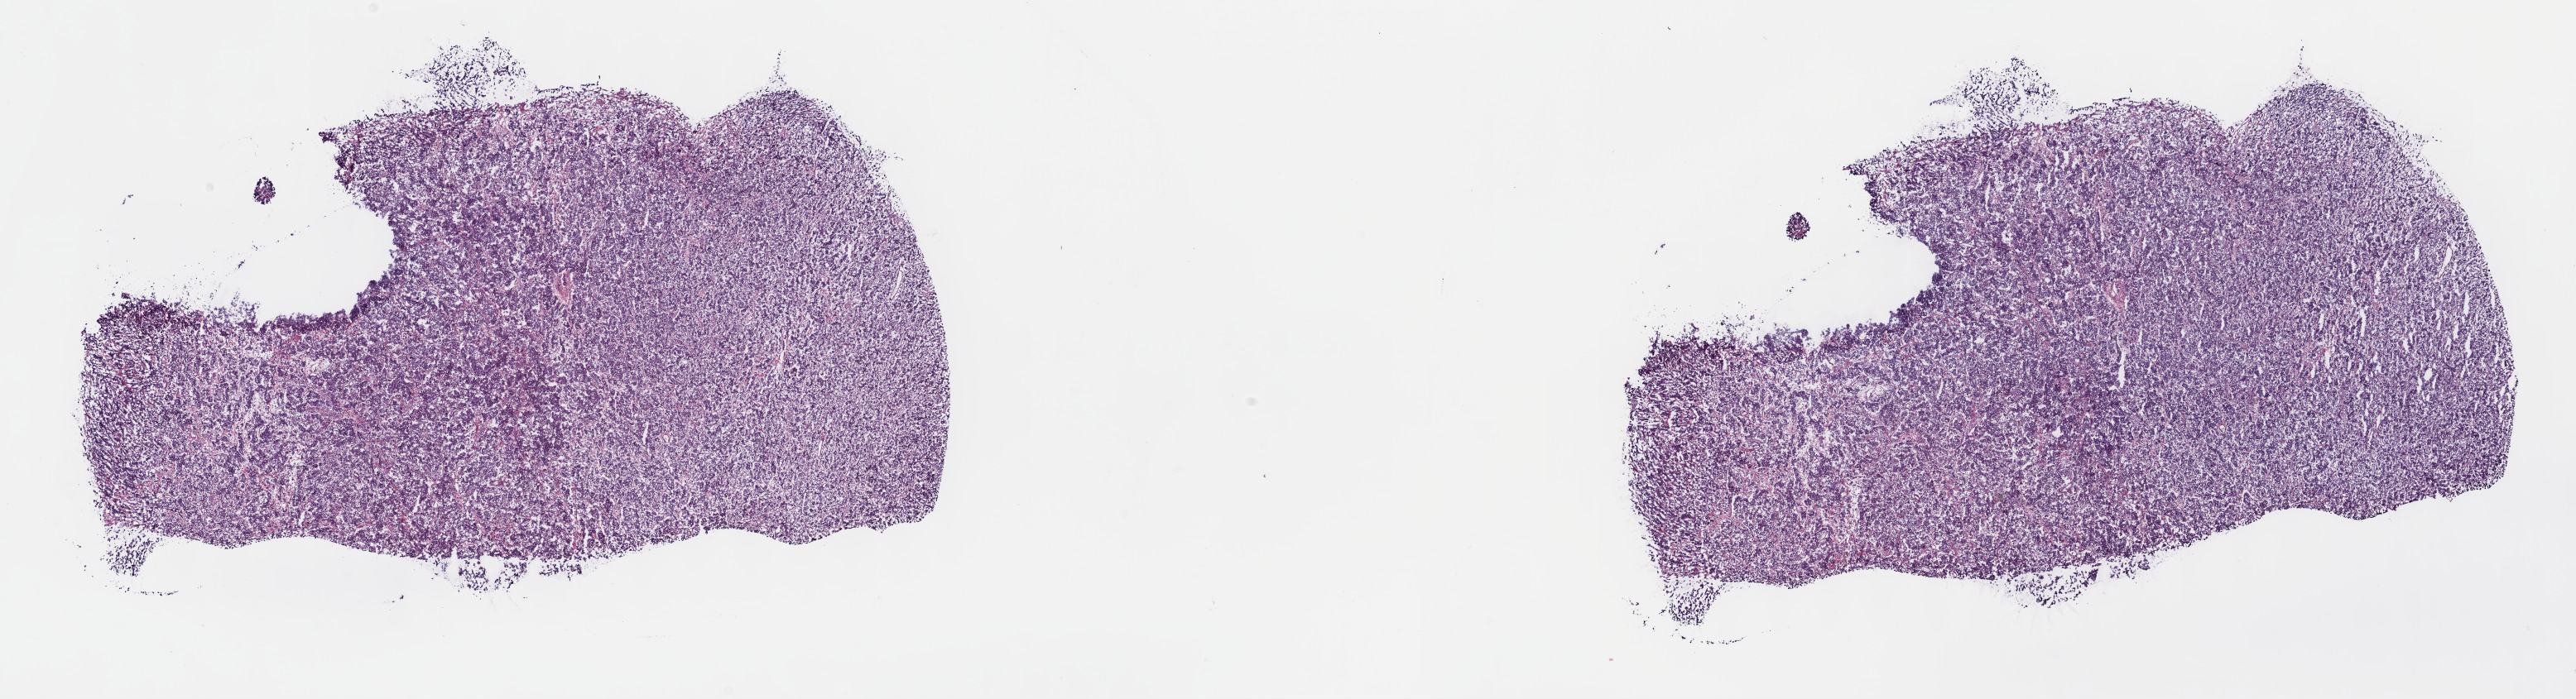
Digitized H&E-stained tissue section (whole slide) — a low-resolution overview of the entire scanned area, about 25.2 x 6.8 mm (from a 40x scan); frozen section from the top of the tissue portion; sample: primary tumour, testis. Male, age 34 years at initial diagnosis. Composition of this section per pathologist review: tumour cells 80%, tumour nuclei 80%, normal cells 0%, stromal cells 10%, necrosis 10%. Inflammatory infiltration, as recorded: lymphocyte infiltration 40%, monocyte infiltration 20%, neutrophil infiltration 20%.
• pathologic diagnosis: Seminoma, NOS
• AJCC pathologic stage: IS (7th edition)
• laterality: left
• TNM: T2 N0 M0